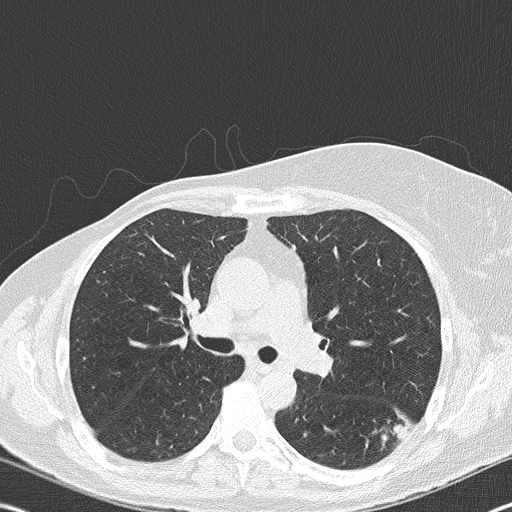
Low-dose screening chest CT, axial slice; second screening round (one year after baseline); lung window (W 1500 / L -600 HU); 2 mm slice thickness; lung (sharp) reconstruction kernel (B50f); slice 113 of 177 in the series; 512 × 512 image matrix, field of view 342 × 342 mm. Female participant, aged 60 years at enrolment.
Lesion marked by an expert reader, box from (x=362, y=390) to (x=427, y=450) px. Reader record for this screening exam (exam-level; its link to the box is not recorded): non-calcified nodule or mass ≥4 mm, left lower lobe, 18 × 16 mm, spiculated (stellate) margins, soft tissue attenuation, pre-existing on the prior screen: no. Participant outcome: lung cancer diagnosed 35 days after this screen — carcinoma, NOS, left hilum, stage IV (AJCC 6th edition), 45 mm at pathology.